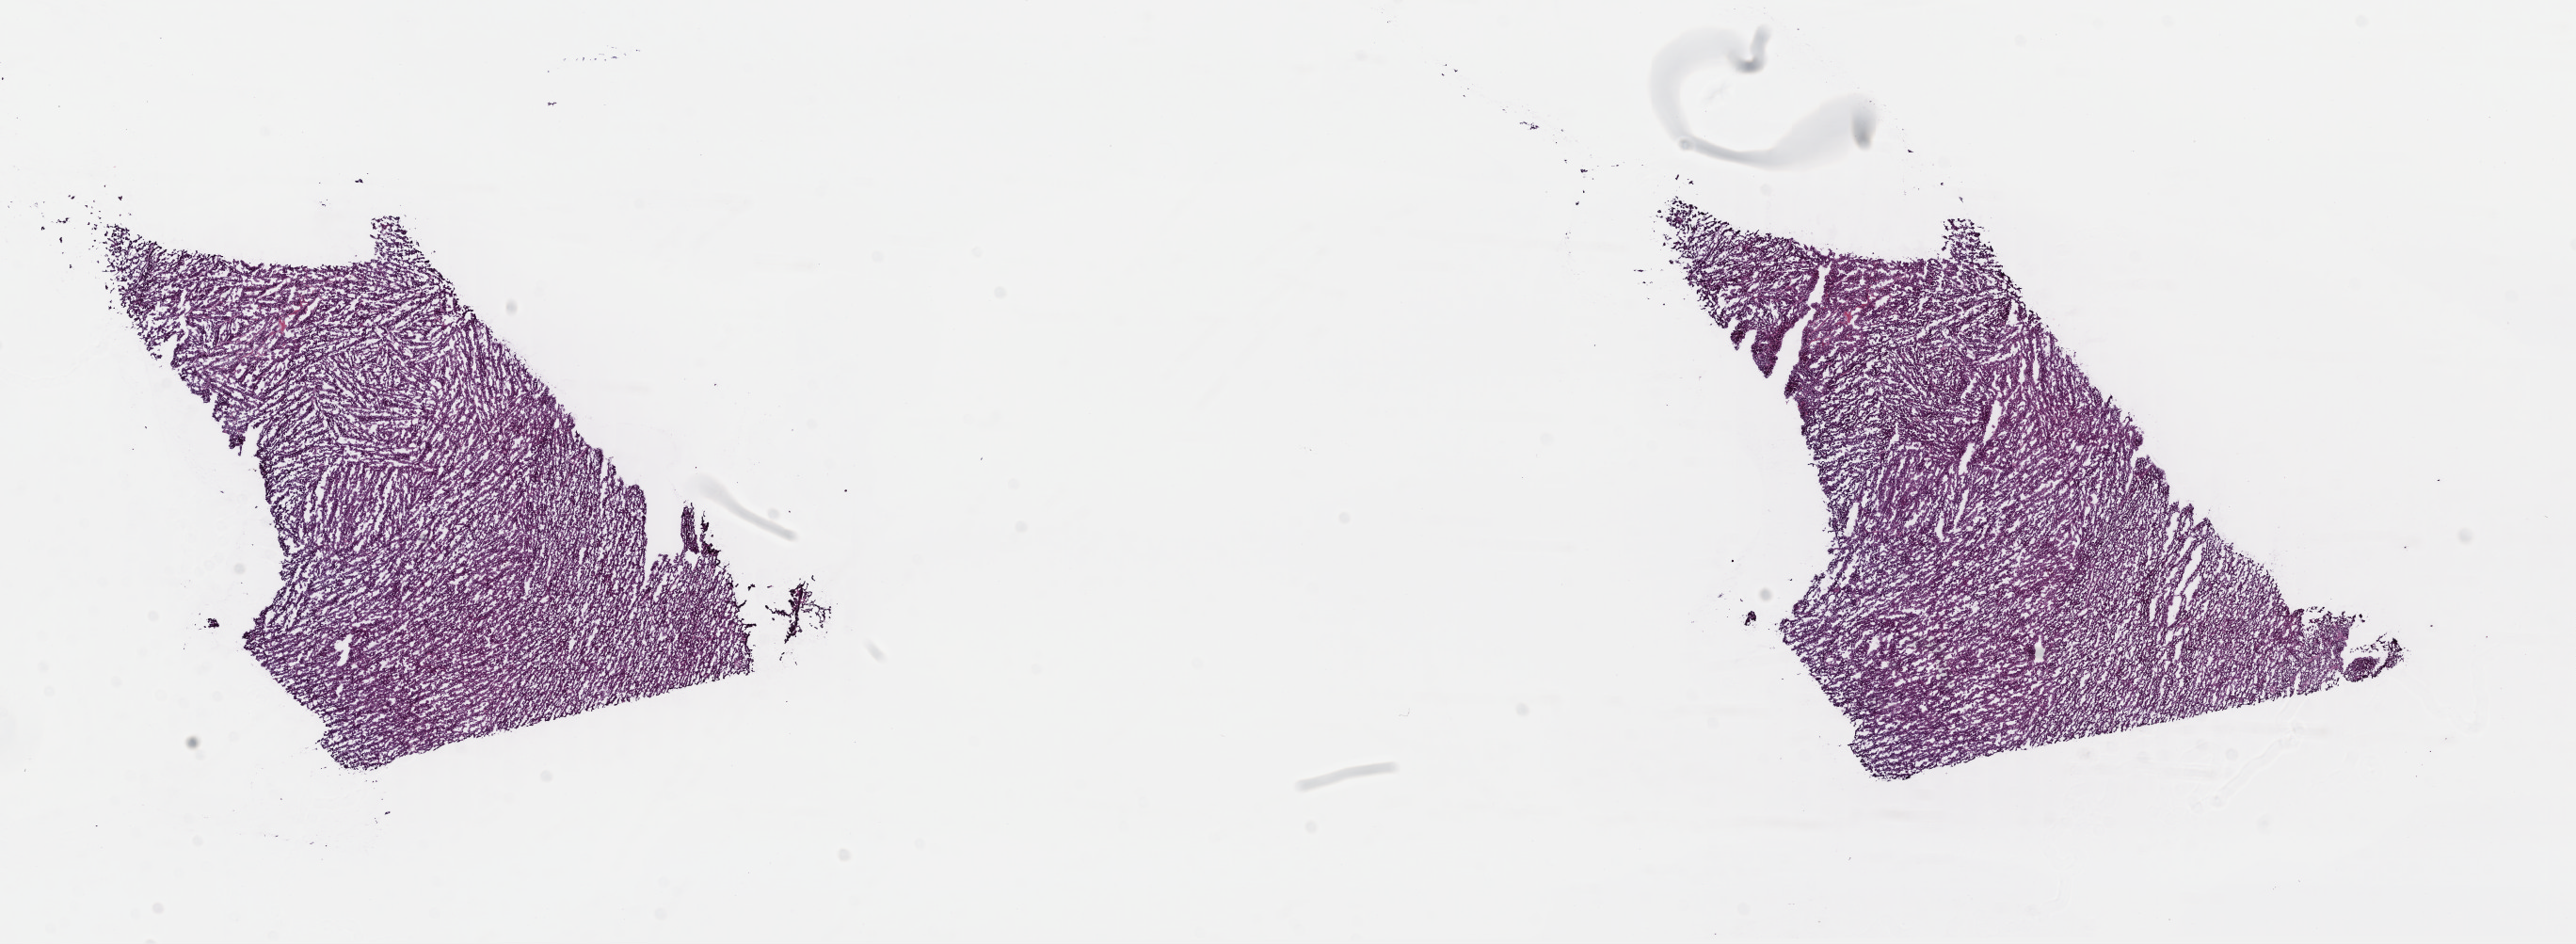
Digitized H&E tissue section (whole slide), low-resolution overview of the scanned area, about 21.5 x 7.9 mm, frozen section, primary tumour sample from the adrenal cortex. Male, age 39 years at initial diagnosis. Composition of this section per pathologist review: tumour cells 100%, tumour nuclei 97%, normal cells 0%, stromal cells 0%, necrosis 0%. Infiltration values recorded for this section: lymphocyte infiltration 0%, monocyte infiltration 0%, neutrophil infiltration 0%.
Laterality: right. Pathologic diagnosis: Adrenal cortical carcinoma (cortex of adrenal gland).